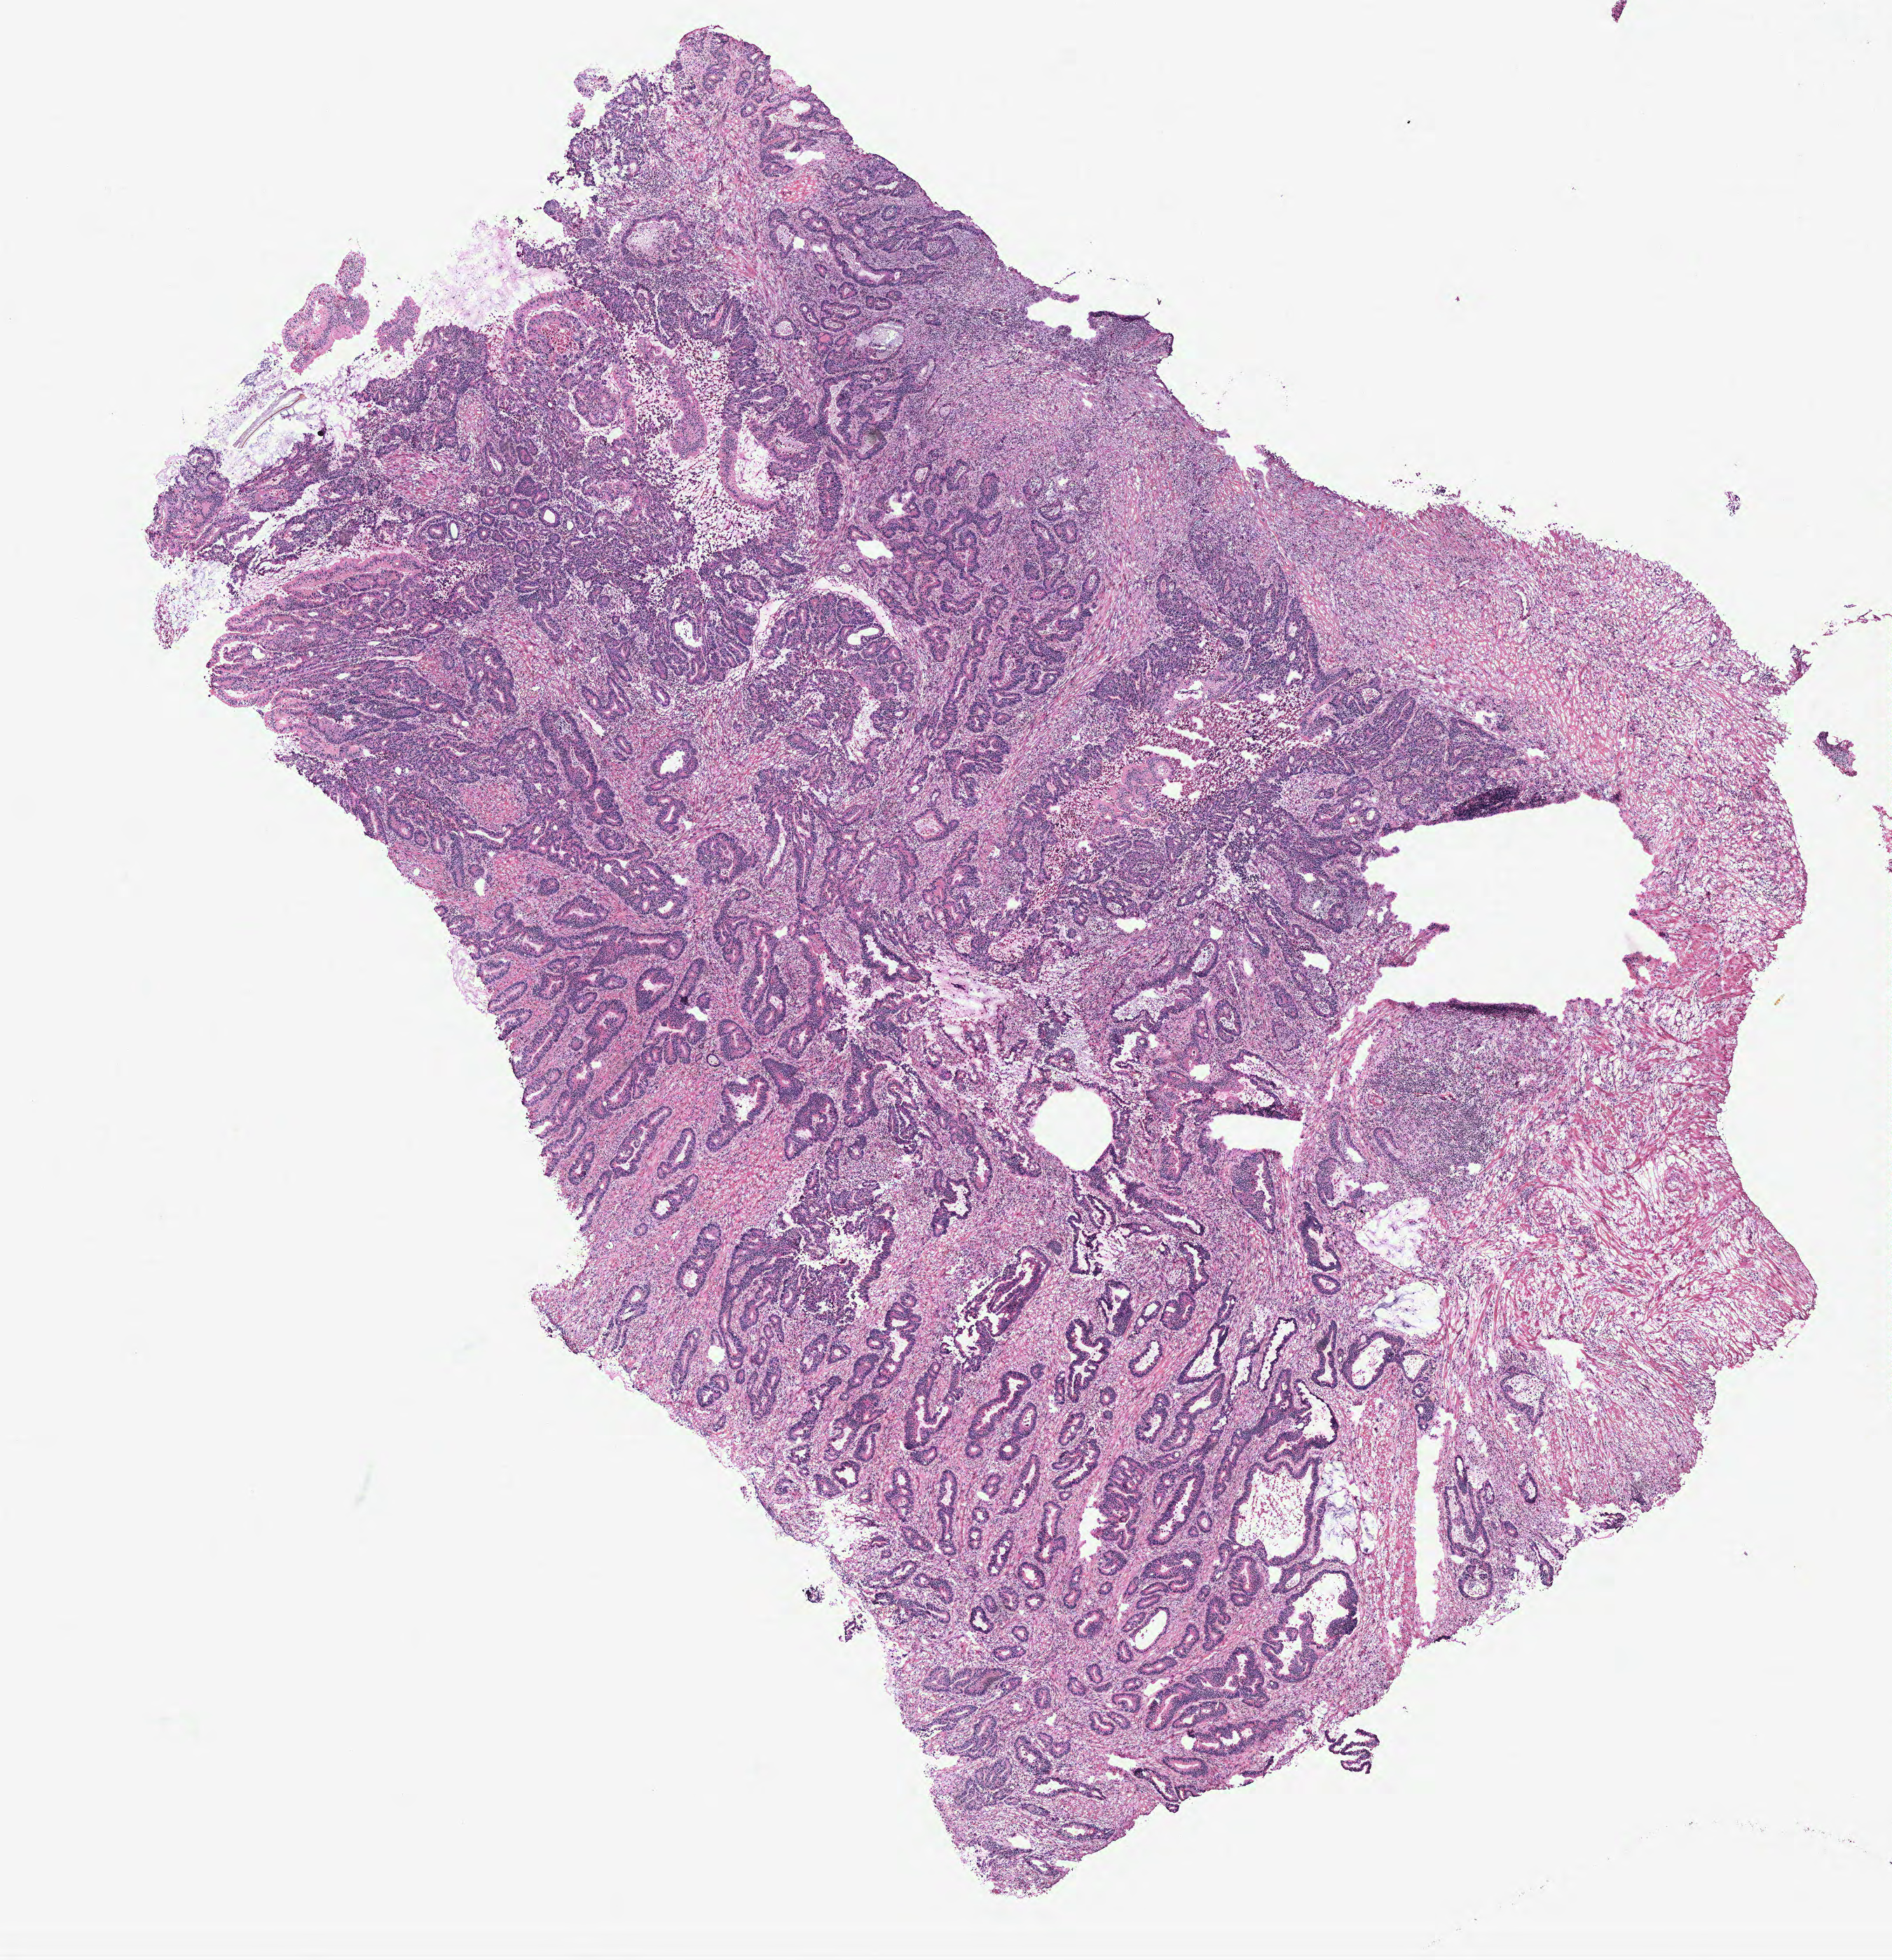
Digitized H&E-stained tissue section (whole slide) — shown as a low-resolution overview of the whole scanned area (about 10.8 x 11.2 mm, from a 40x scan), colon, tumour tissue. 75-year-old female patient.
• primary tumour site (as recorded): colon
• AJCC pathologic stage: IIIB
• histologic diagnosis: Adenocarcinoma, NOS